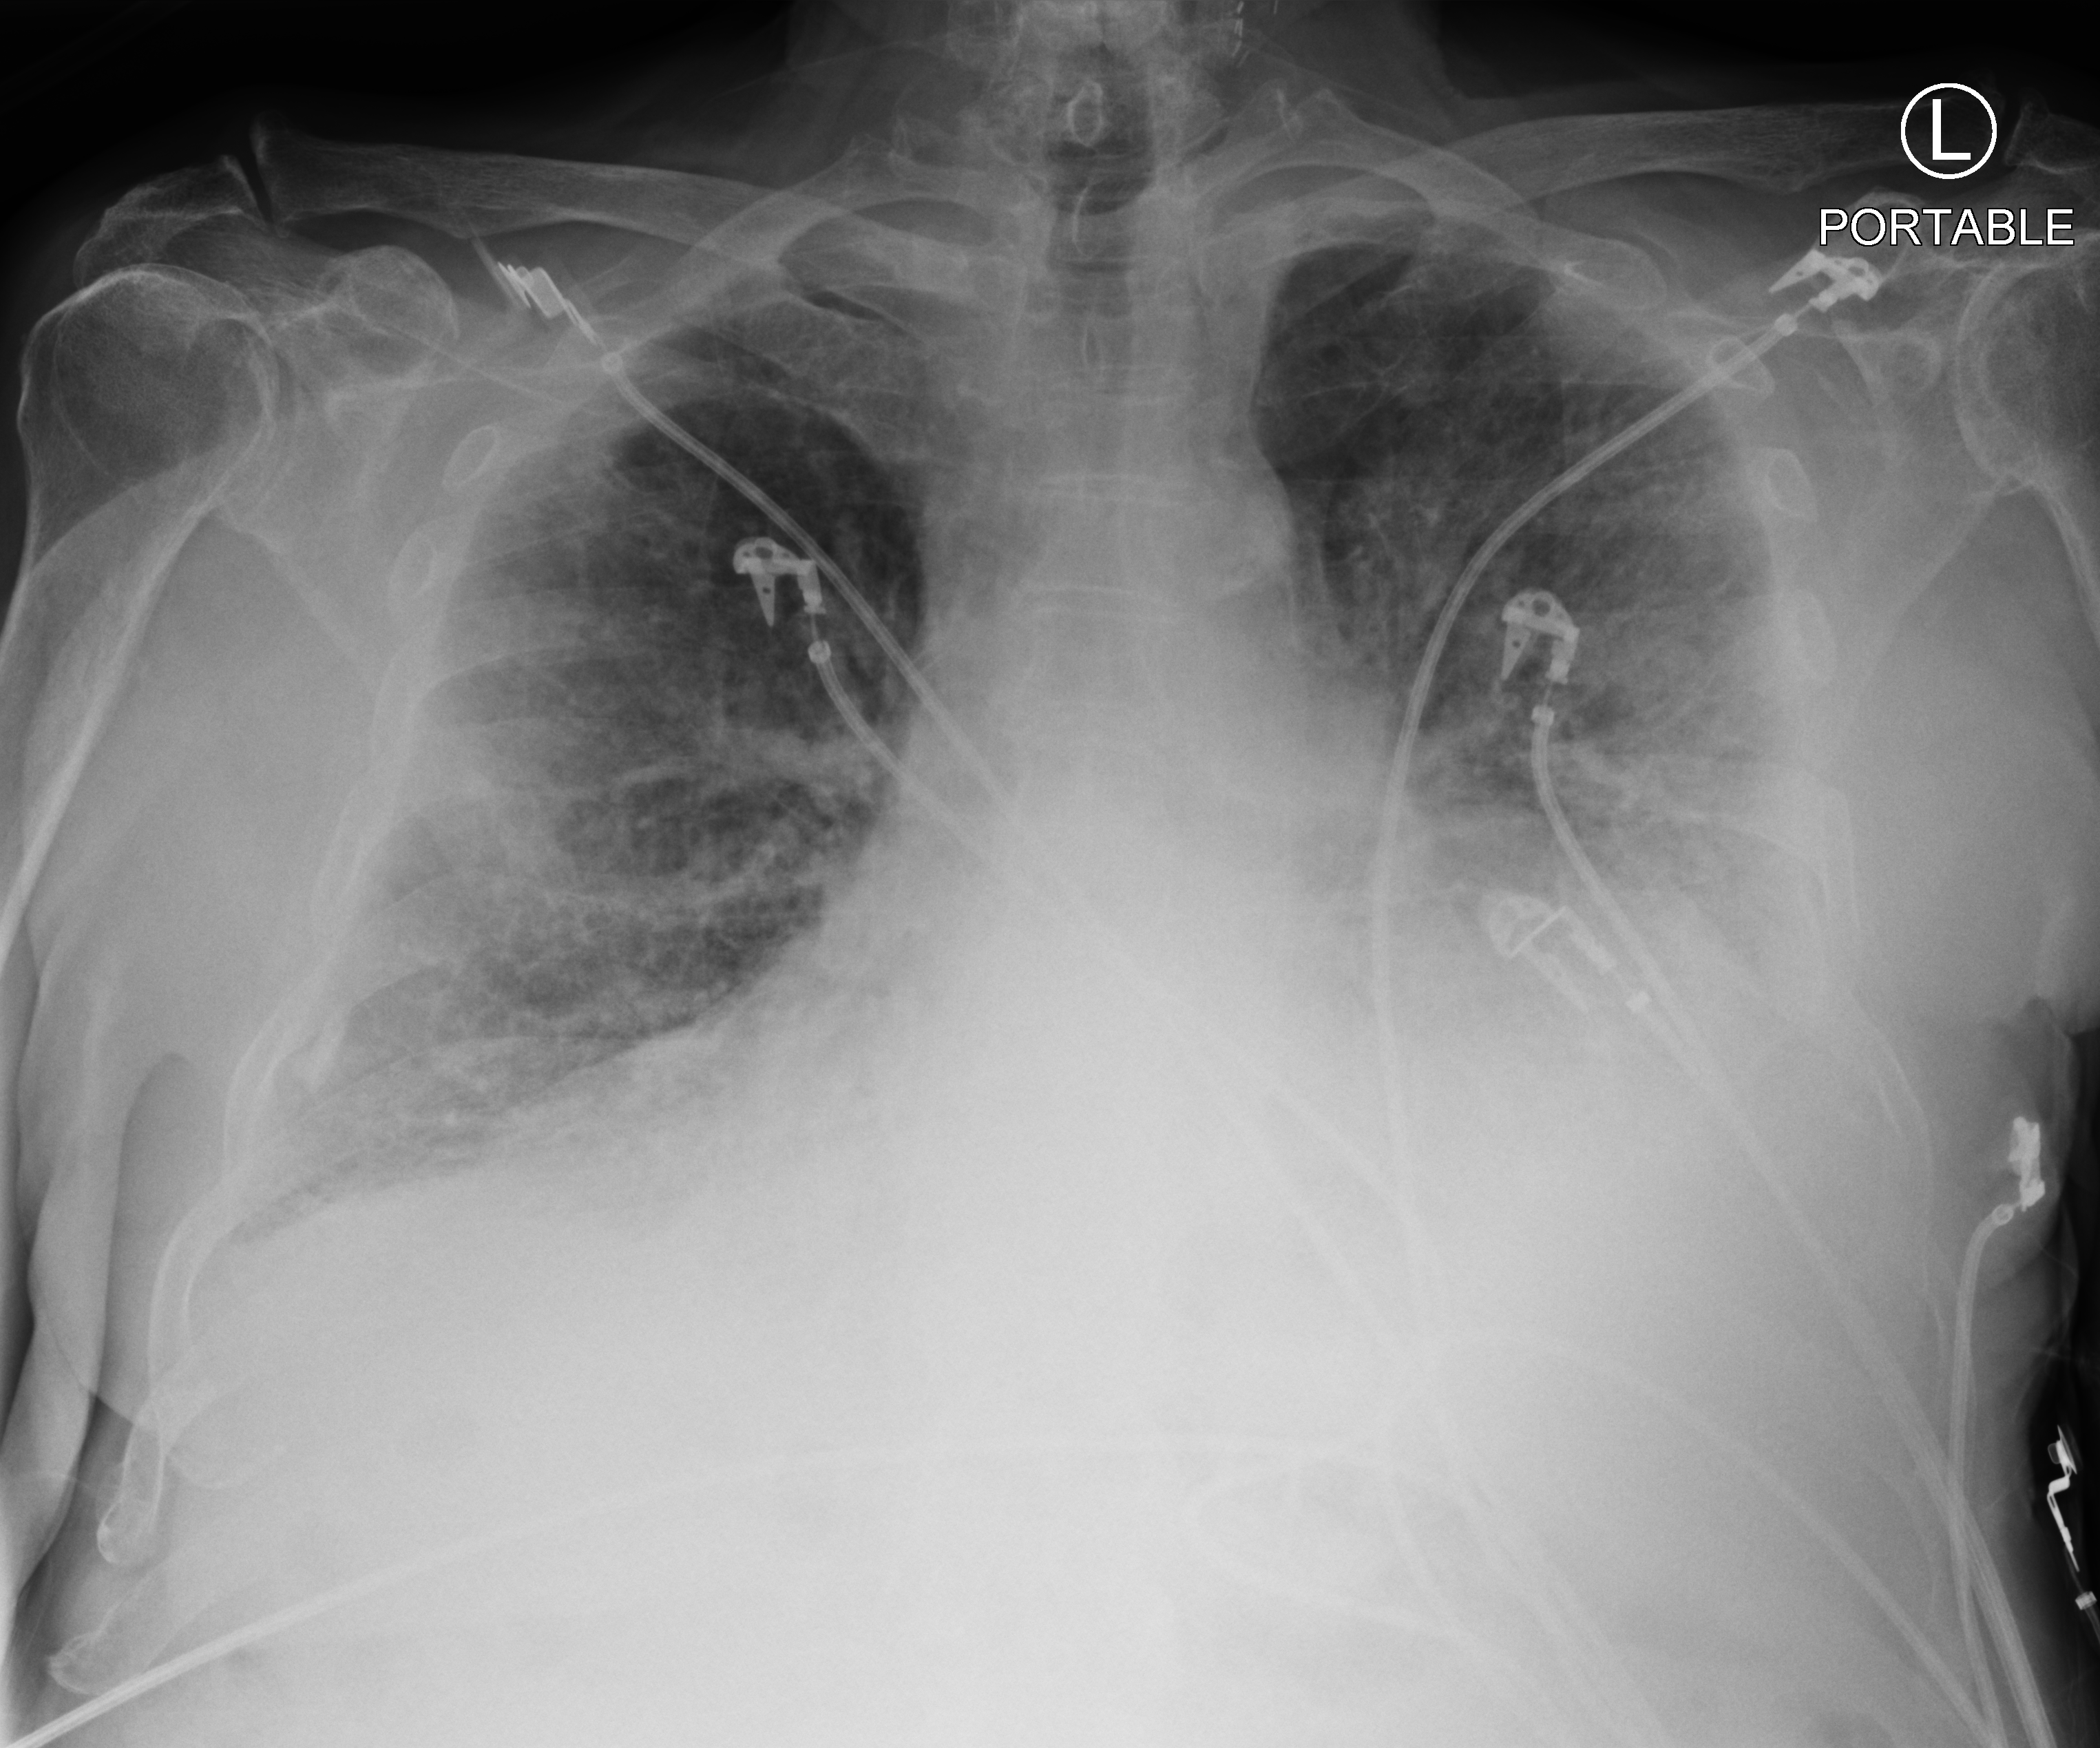
Portable chest radiograph. Male patient hospitalised with COVID-19, age 75–90 years.
Hospital-stay facts (about this admission, not read from this image; timing relative to this image not recorded): mechanically ventilated during this hospital stay: yes; admitted to intensive care during this hospital stay: yes.